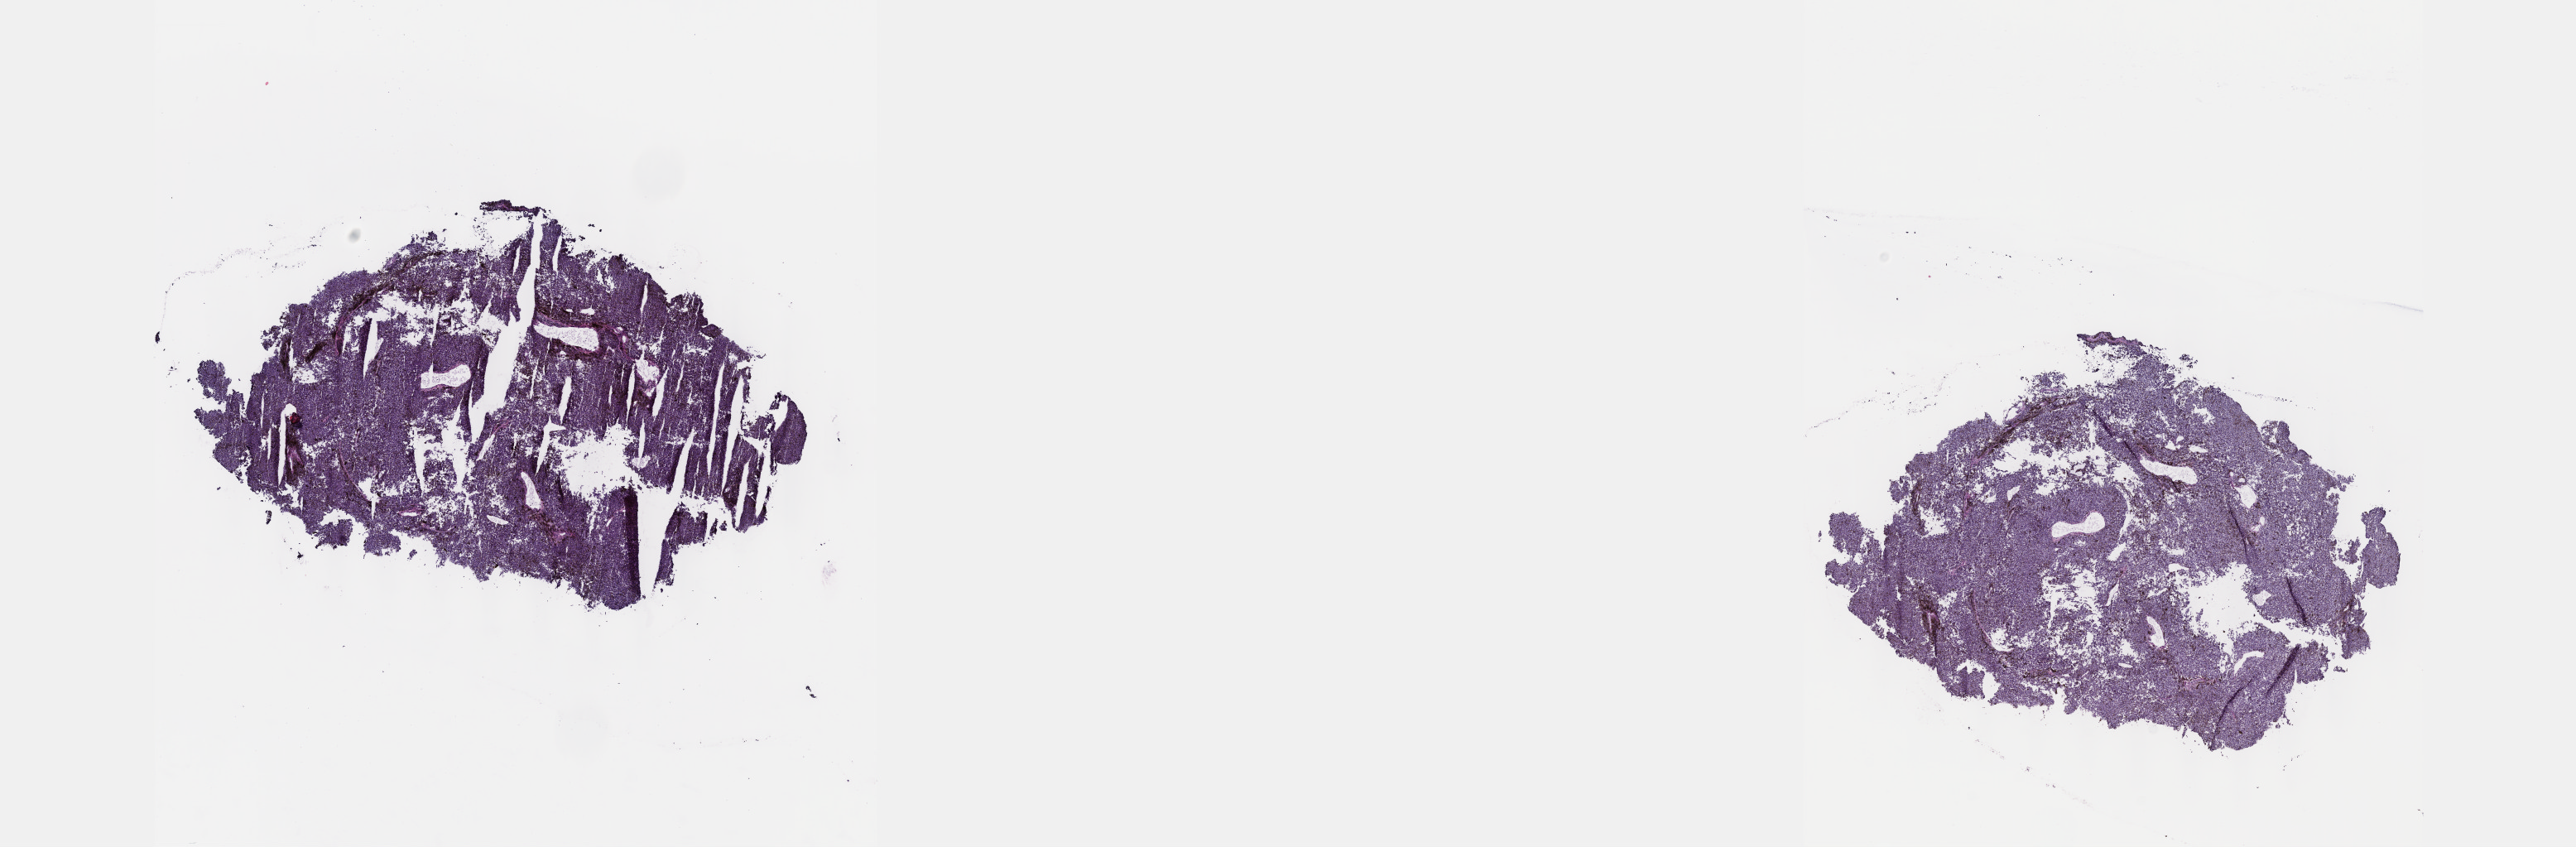
Digitized H&E-stained tissue section (whole slide), a low-resolution overview of the entire scanned area, about 25.1 x 8.3 mm; frozen section from the top of the tissue portion; sample: primary tumour, uvea. Male patient; age at initial diagnosis 50 years. Pathologist review of this section (percent, as recorded): tumour cells 100%, tumour nuclei 80%, normal cells 0%, stromal cells 0%, necrosis 0%. Infiltration values recorded for this section: lymphocyte infiltration 2%, monocyte infiltration 0%, neutrophil infiltration 0%.
• AJCC pathologic stage: IIIA (7th edition)
• TNM: T4a N0 M0
• pathologic diagnosis: Spindle cell melanoma, NOS (choroid)